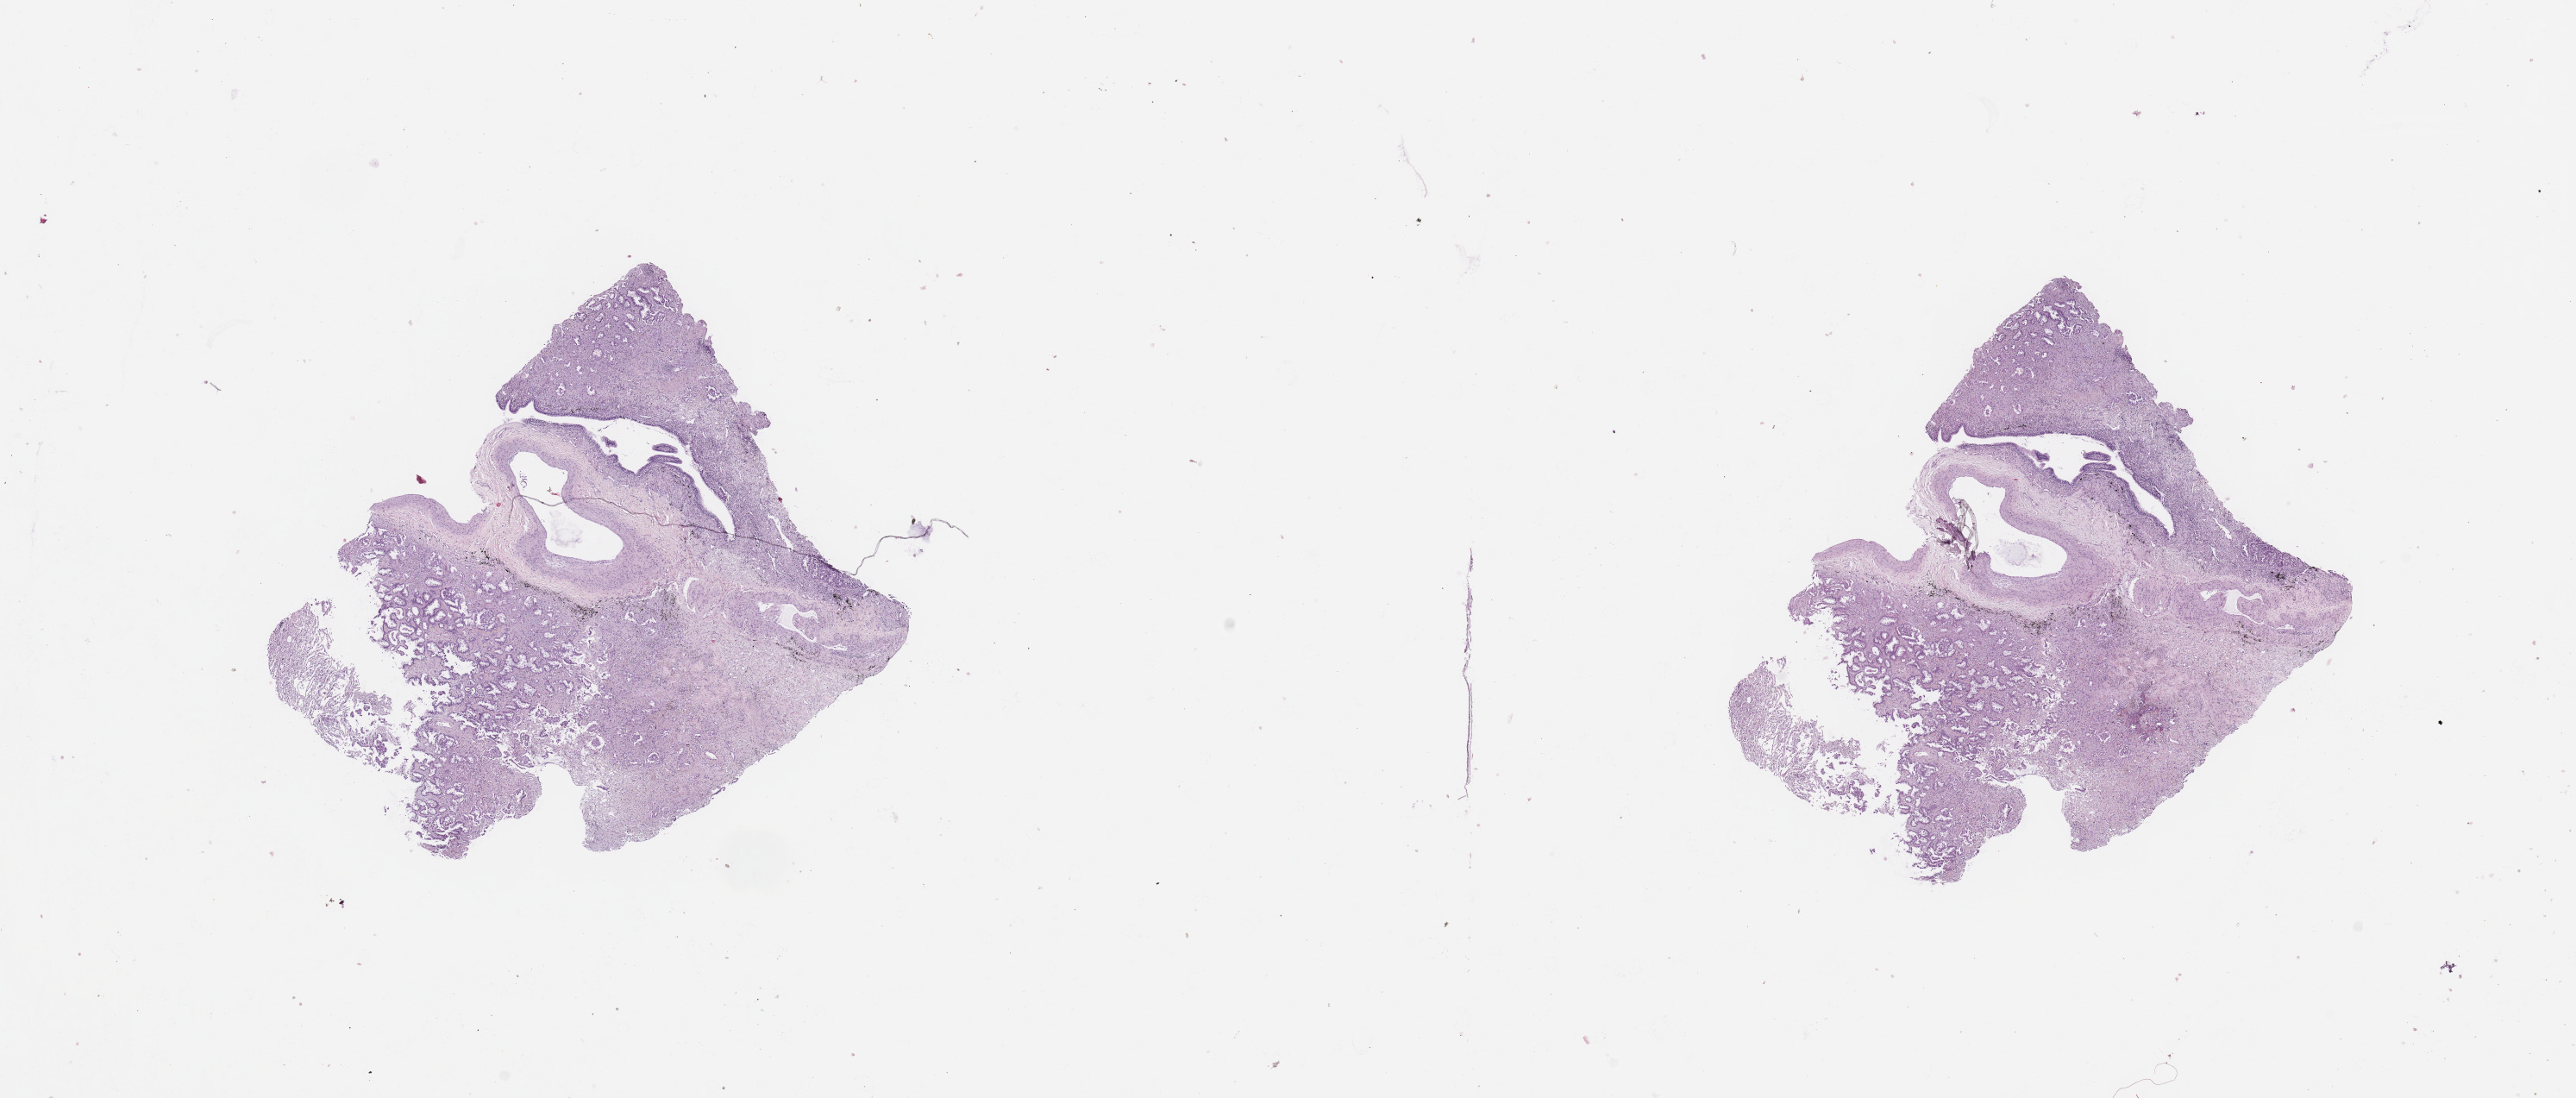
Digitized Hematoxylin and eosin (H&E) stained tissue section (whole slide) — shown as a low-resolution overview of the whole scanned area (about 23.6 x 10.1 mm, from a 20x scan). Tumour tissue sample, lung. Patient: male, age 77 years.
Diagnosis: Adenocarcinoma, NOS.